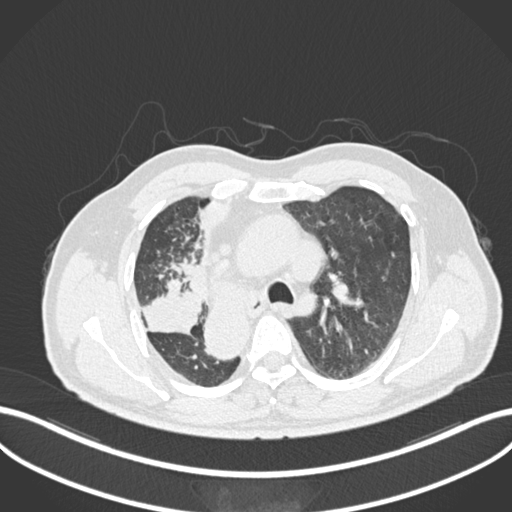
Chest CT, one axial slice; slice 163 of 206 in the series (ordered by position); lung window (W 1500 / L -600 HU); 1 mm slice thickness; 512 × 512 image matrix, field of view 400 × 400 mm. Patient: male, 67 years. Case-level facts recorded for this patient, not image findings: clinical TNM (as recorded): T2a N0 M0.
Outlined on this slice (bounding box drawn by a radiologist):
- lung tumour (recorded histology: squamous cell carcinoma): bounding box [x1, y1, x2, y2] px = [136, 278, 203, 340]